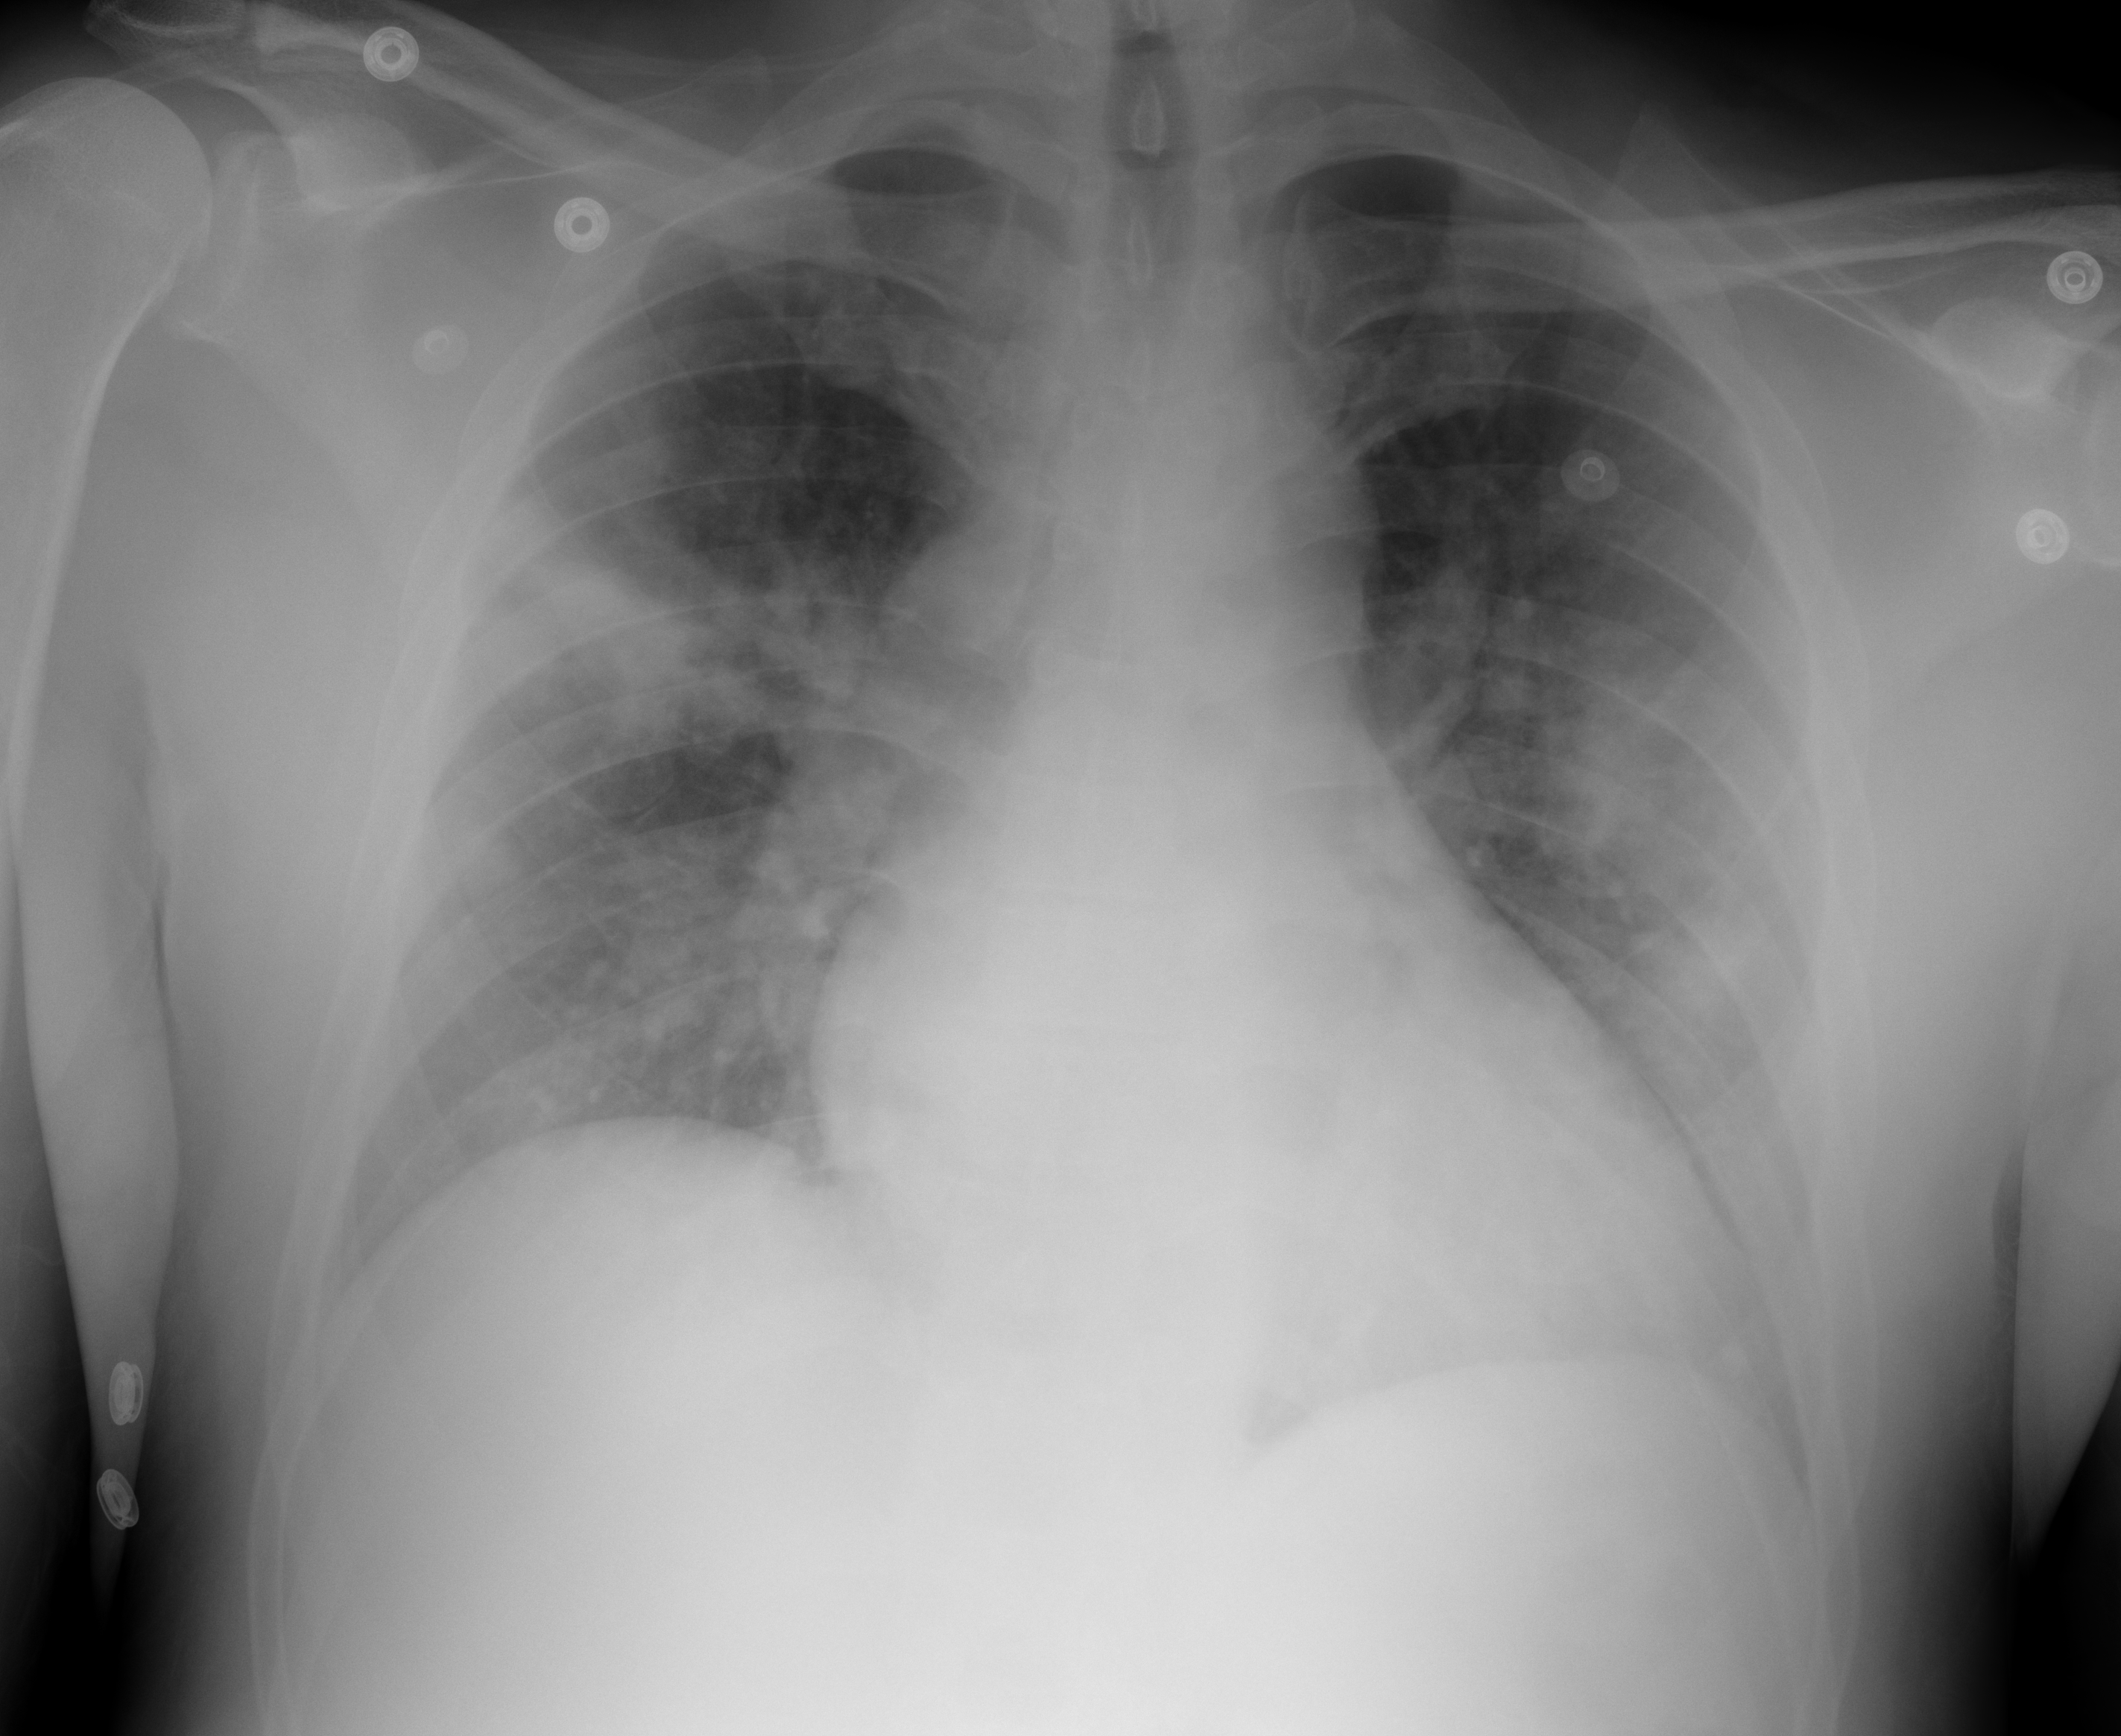
Chest X-ray, AP projection. Male patient, age 48 years; imaged 0 days after the COVID-19 diagnosis.
Radiologist key findings (as recorded): Bilateral patchy airspace disease involving both mid and lower lung zones, left worse than the right.